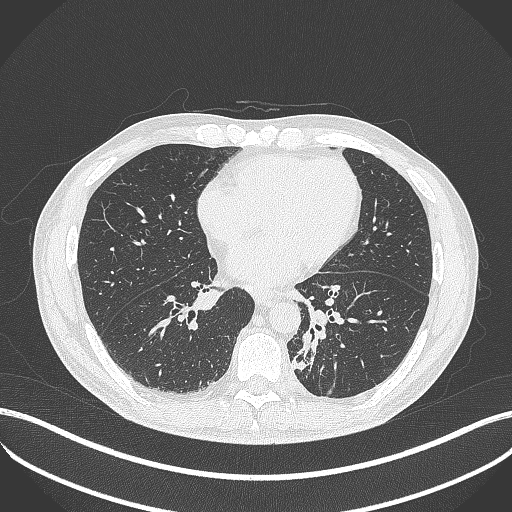
Chest CT, one axial slice. Slice 161 of 451 in the series (ordered by position). 120 kVp. Lung window (W 1500 / L -600 HU). 1 mm slice thickness. 512 × 512 image matrix, field of view 400 × 400 mm. Patient: male, 72 years. Case-level facts recorded for this patient, not image findings: clinical TNM (as recorded): T2b N0 M1.
Annotated regions visible in this slice (bounding box drawn by a radiologist):
- lung tumour (recorded histology: adenocarcinoma): bounding box [x1, y1, x2, y2] px = [291, 325, 323, 375]